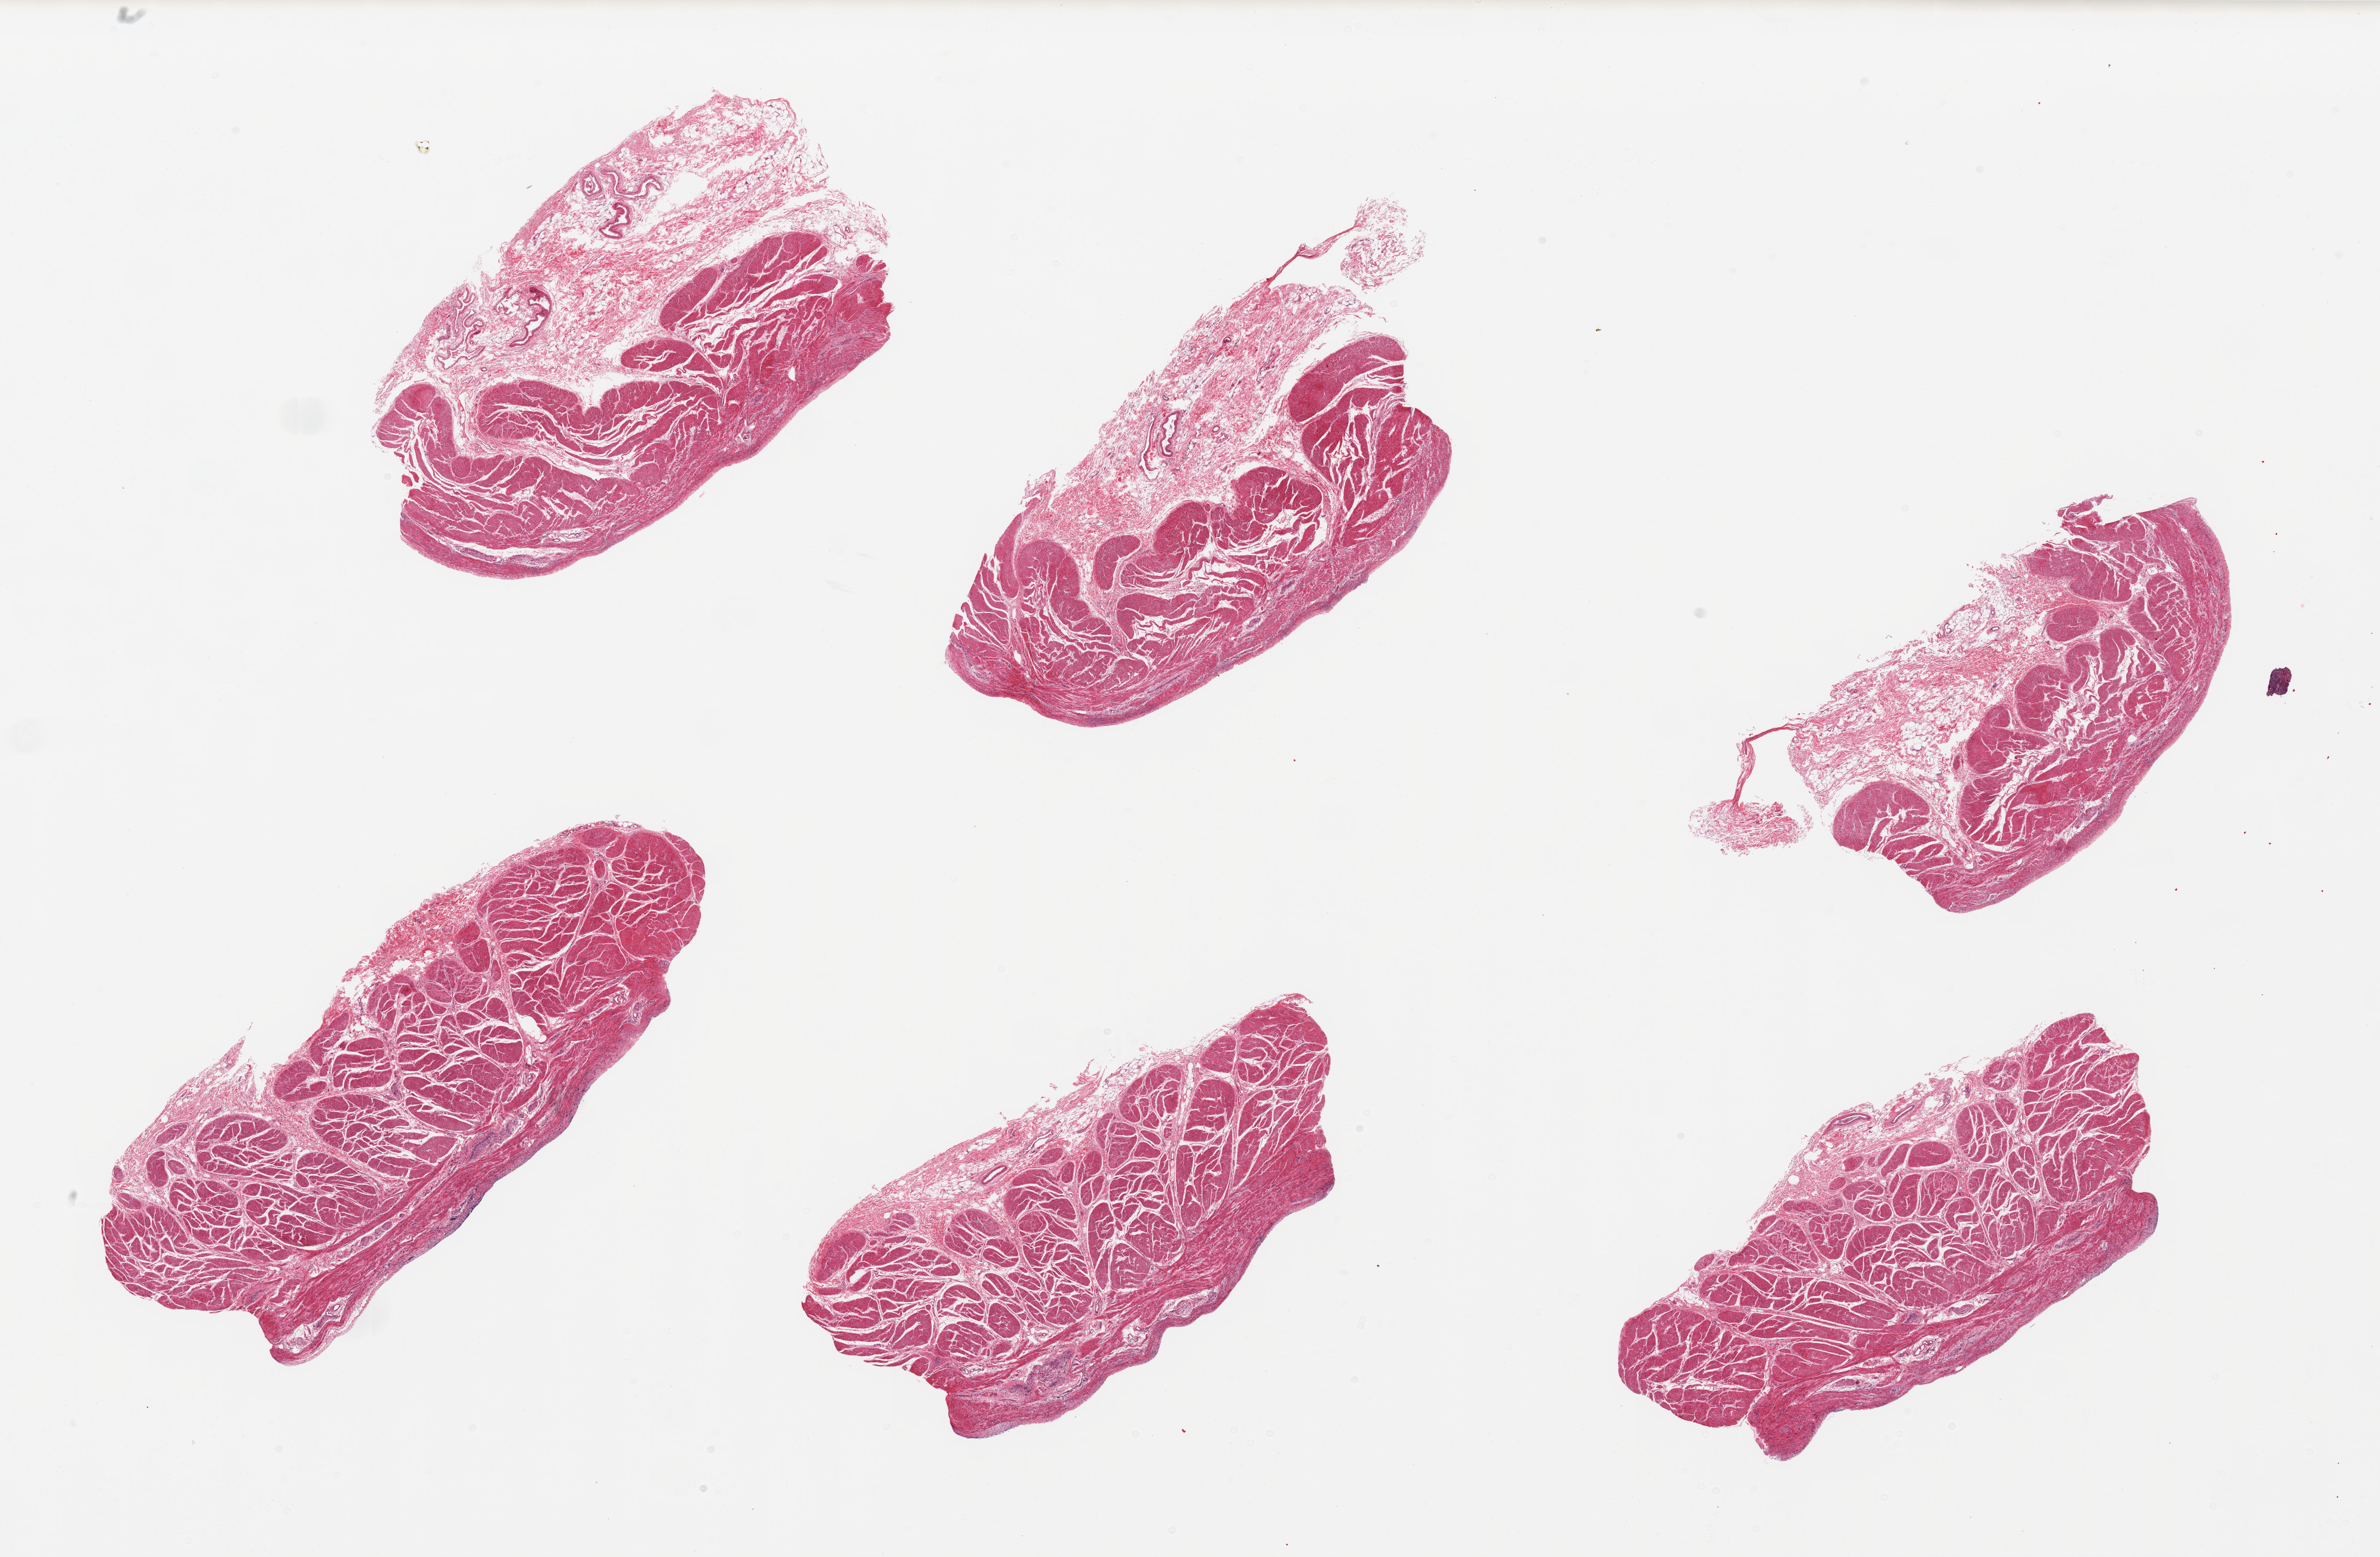
Whole-slide image, haematoxylin and eosin stain — whole scanned area (about 31.5 x 20.6 mm, from a 20x scan) shown as a low-resolution overview, PAXgene-fixed, paraffin-embedded tissue, section of stomach (target tissue), donor tissue sample. Donor sex: male.
Review note (as recorded): 6 pieces; mucosa missing on all pieces; only muscularis and submucosa present.